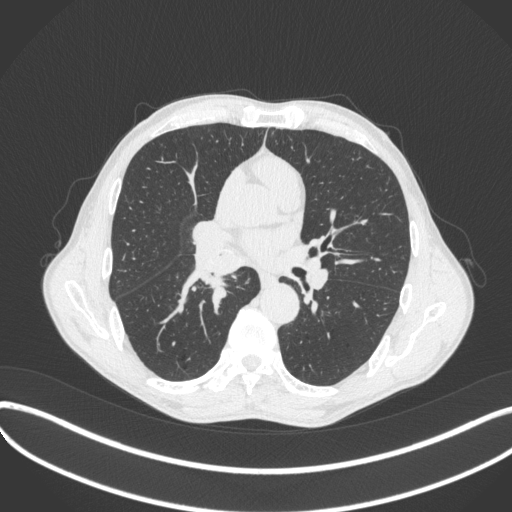
Chest CT, one axial slice. 120 kVp. Lung window (W 1500 / L -600 HU). 1 mm slice thickness. 512 × 512 image matrix, field of view 400 × 400 mm. Patient: male, 65 years. Case-level facts recorded for this patient, not image findings: clinical TNM (as recorded): T2a N0 M0; histopathological grade: G2.
Structures marked on this image (rectangle marked by the reading radiologist):
- lung tumour (recorded histology: squamous cell carcinoma): bounding box [x1, y1, x2, y2] px = [189, 237, 244, 286]